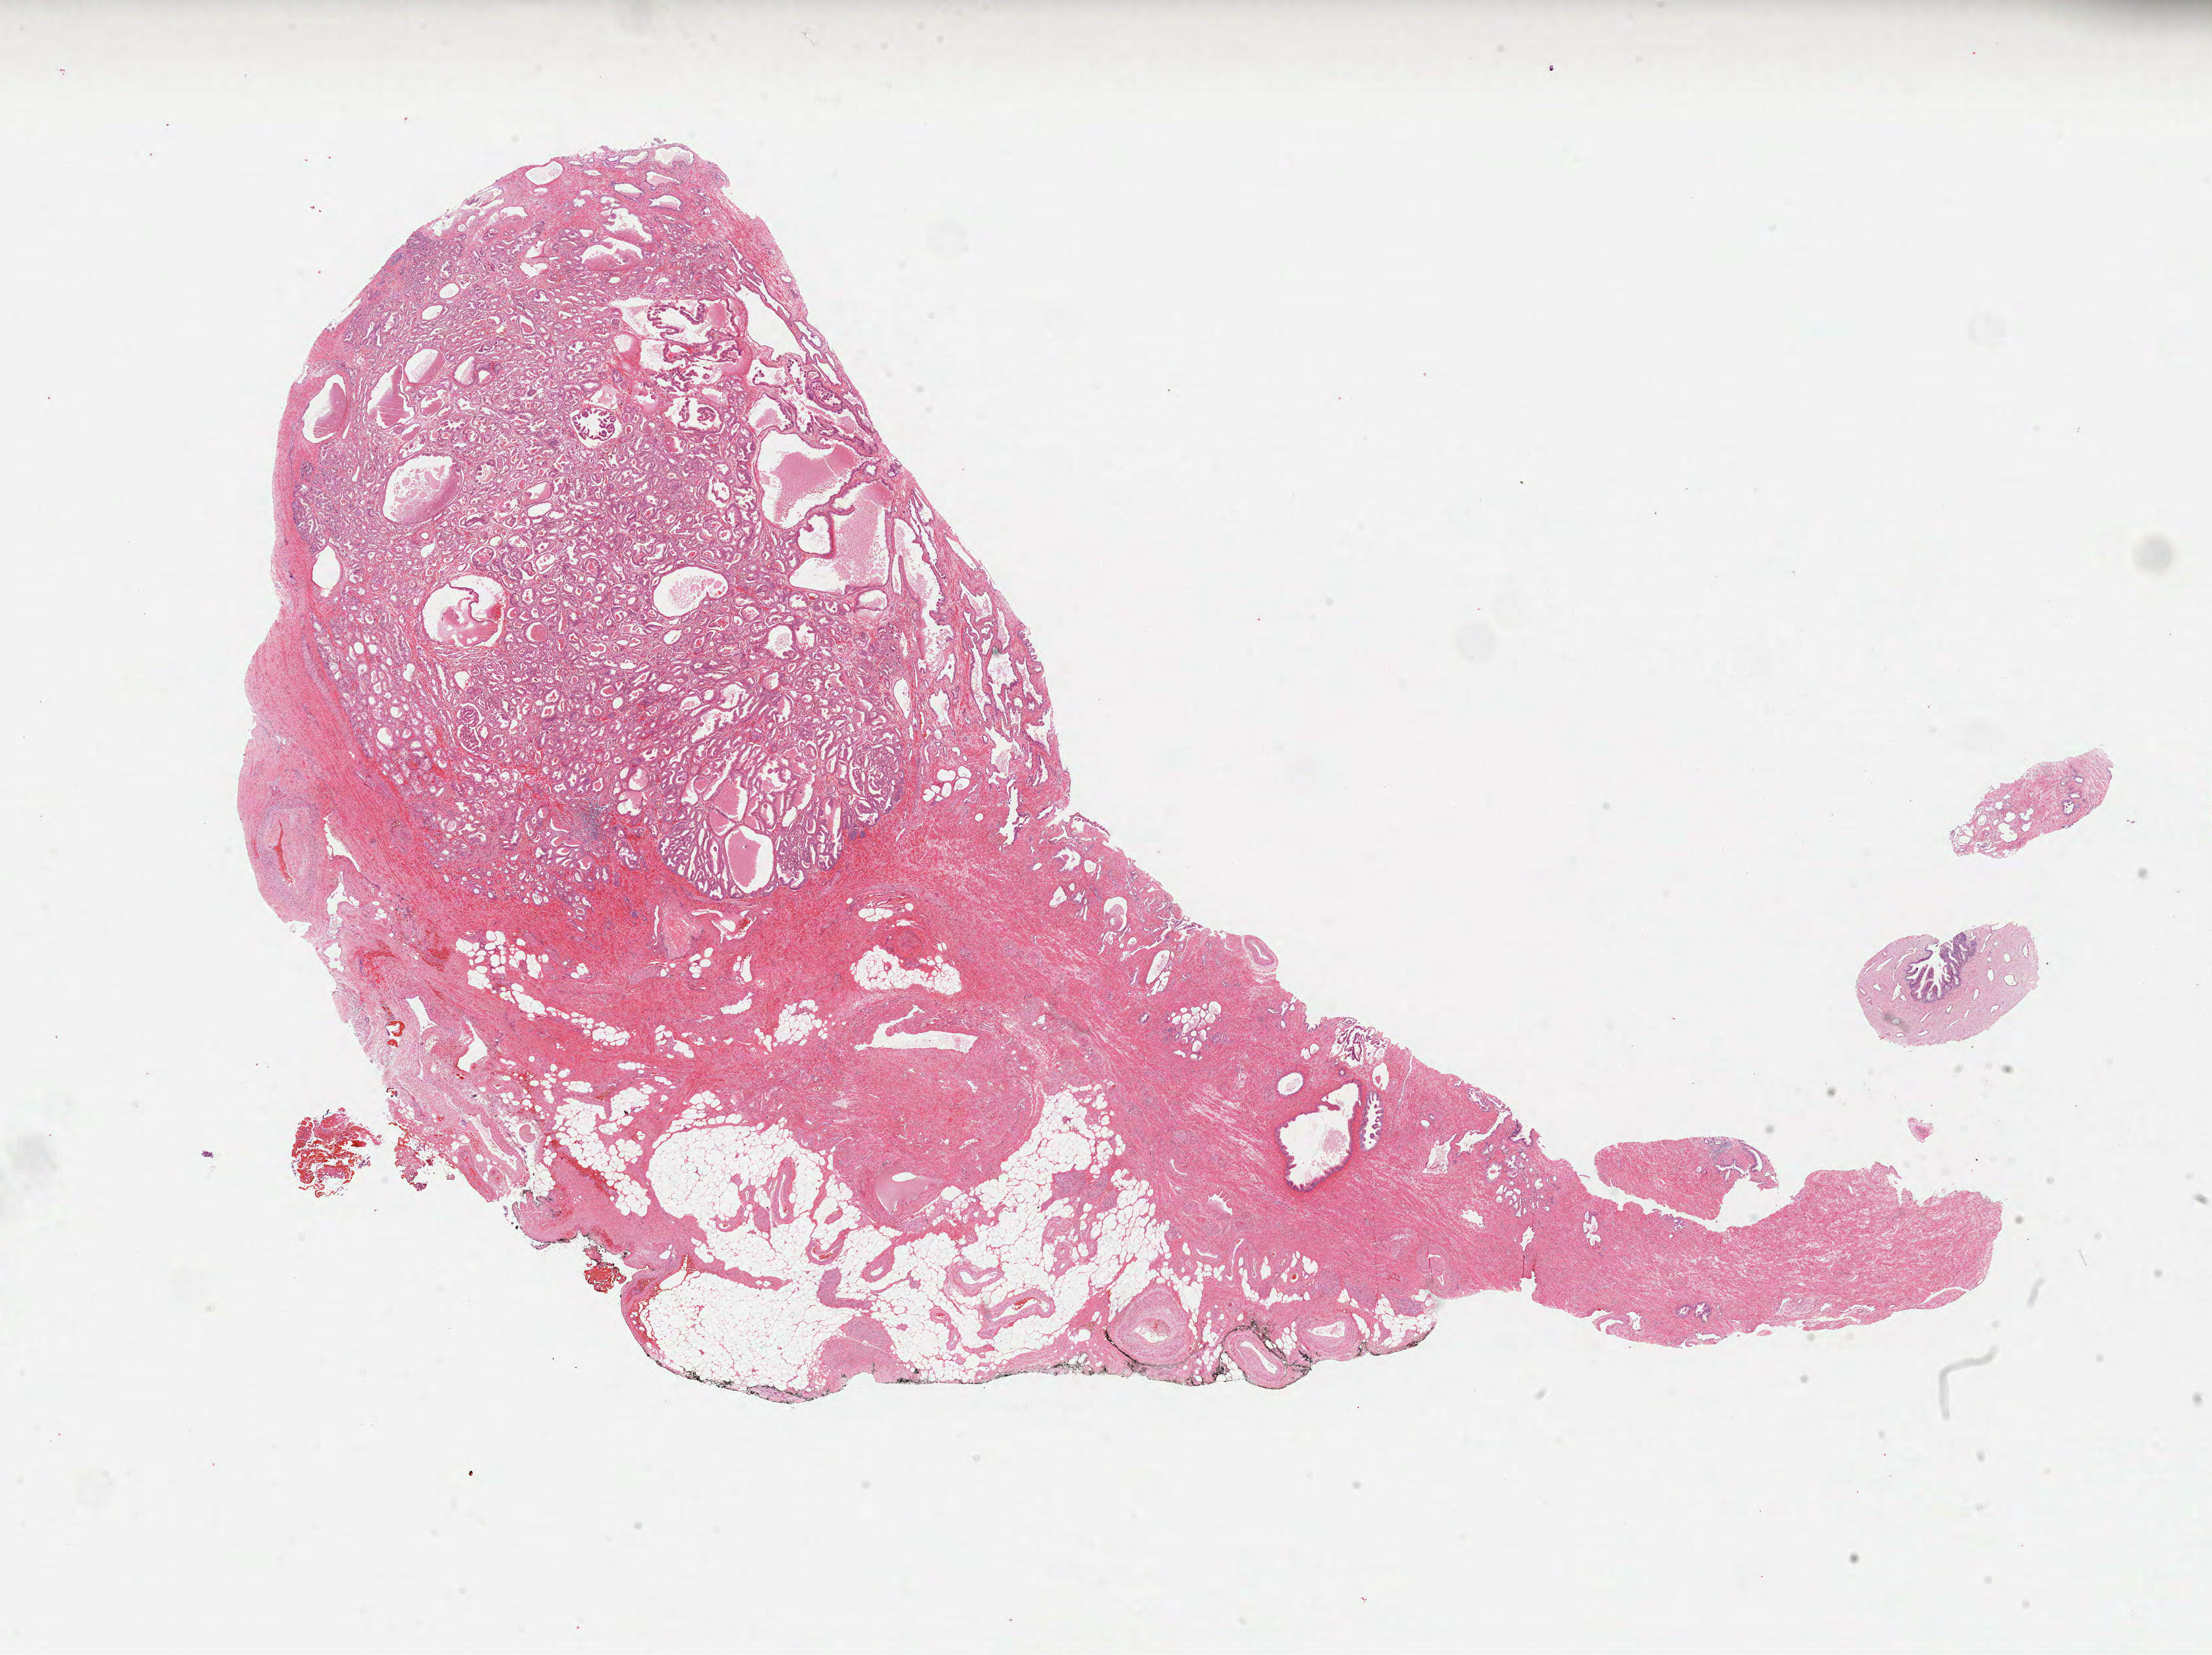
H&E-stained whole-slide image — low-resolution overview of the scanned area, about 27.1 x 20.3 mm (acquisition: 40x scan), formalin-fixed paraffin-embedded (FFPE) diagnostic section, prostate, primary tumour sample. Male, age 62 years at initial diagnosis. Gleason score: 7 (4+3).
* pathologic diagnosis: Acinar cell carcinoma (prostate gland)
* laterality: bilateral